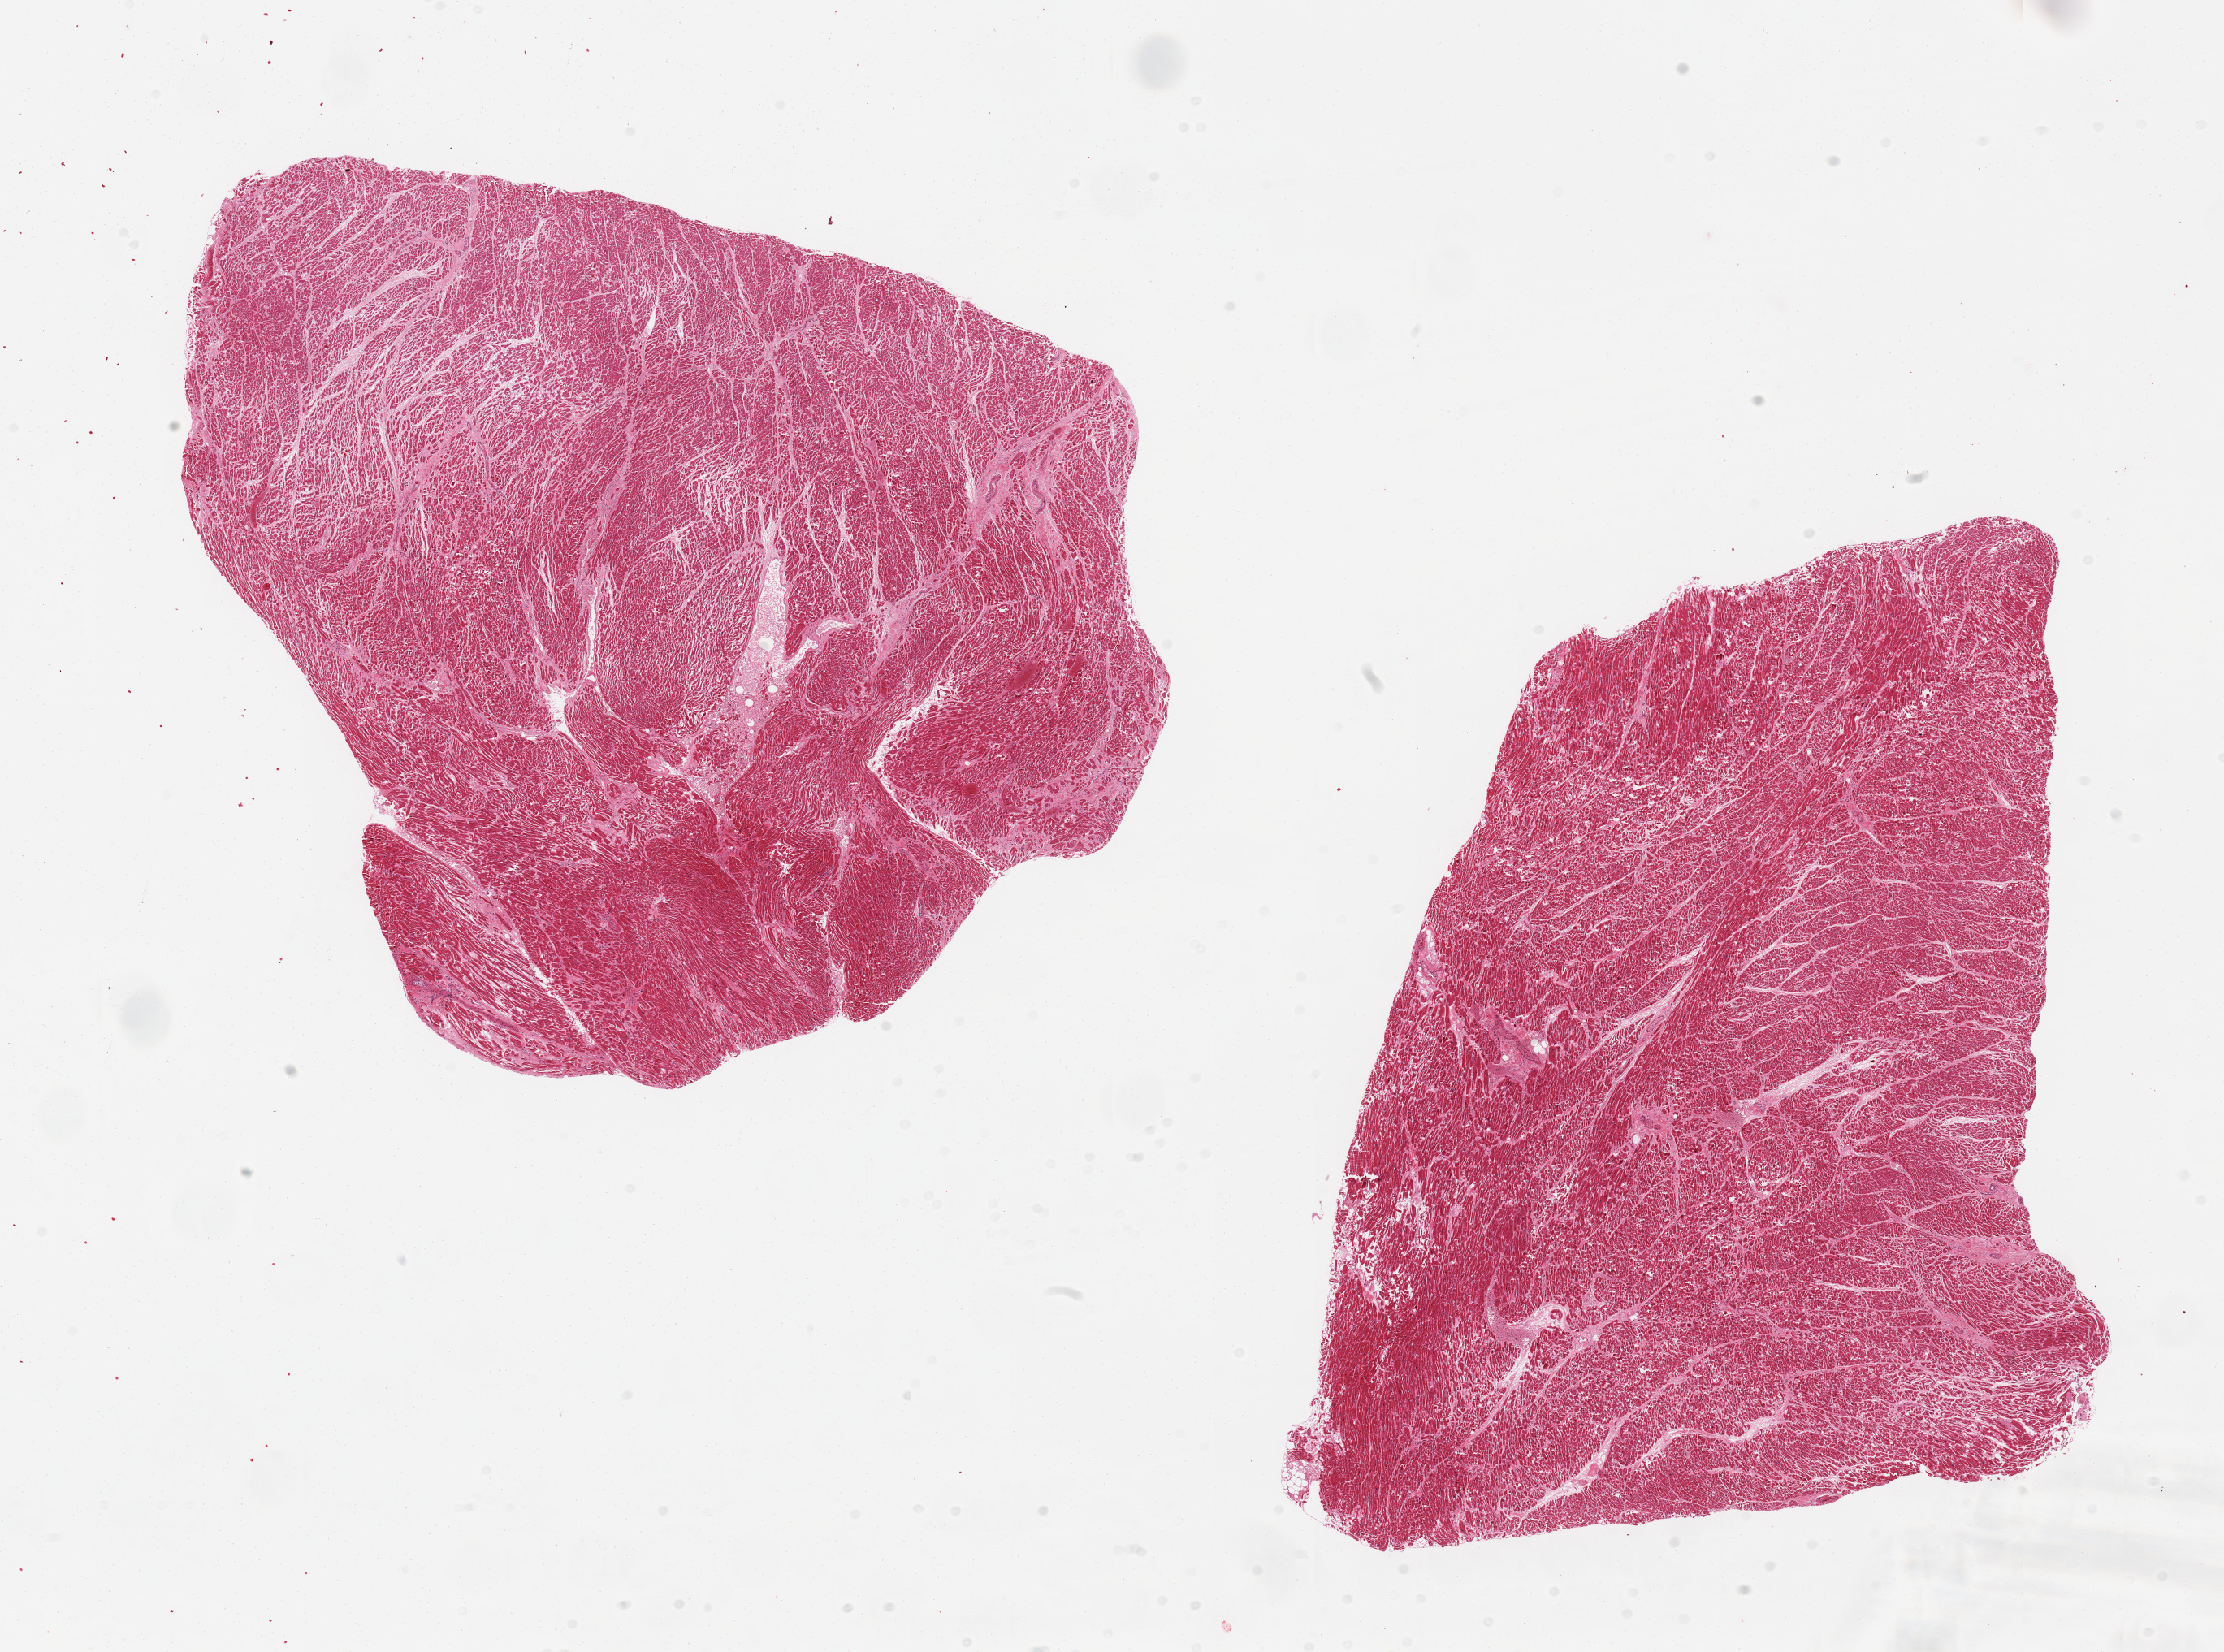
Haematoxylin and eosin whole-slide image, brightfield — shown as a low-resolution overview of the whole scanned area (about 21.7 x 16.1 mm); PAXgene-fixed paraffin-embedded (PFPE) section; target tissue: heart; tissue donor sample.
Pathologist's review note for this sample: 2 pieces, diffuse chronic and subacute ischemic changes.